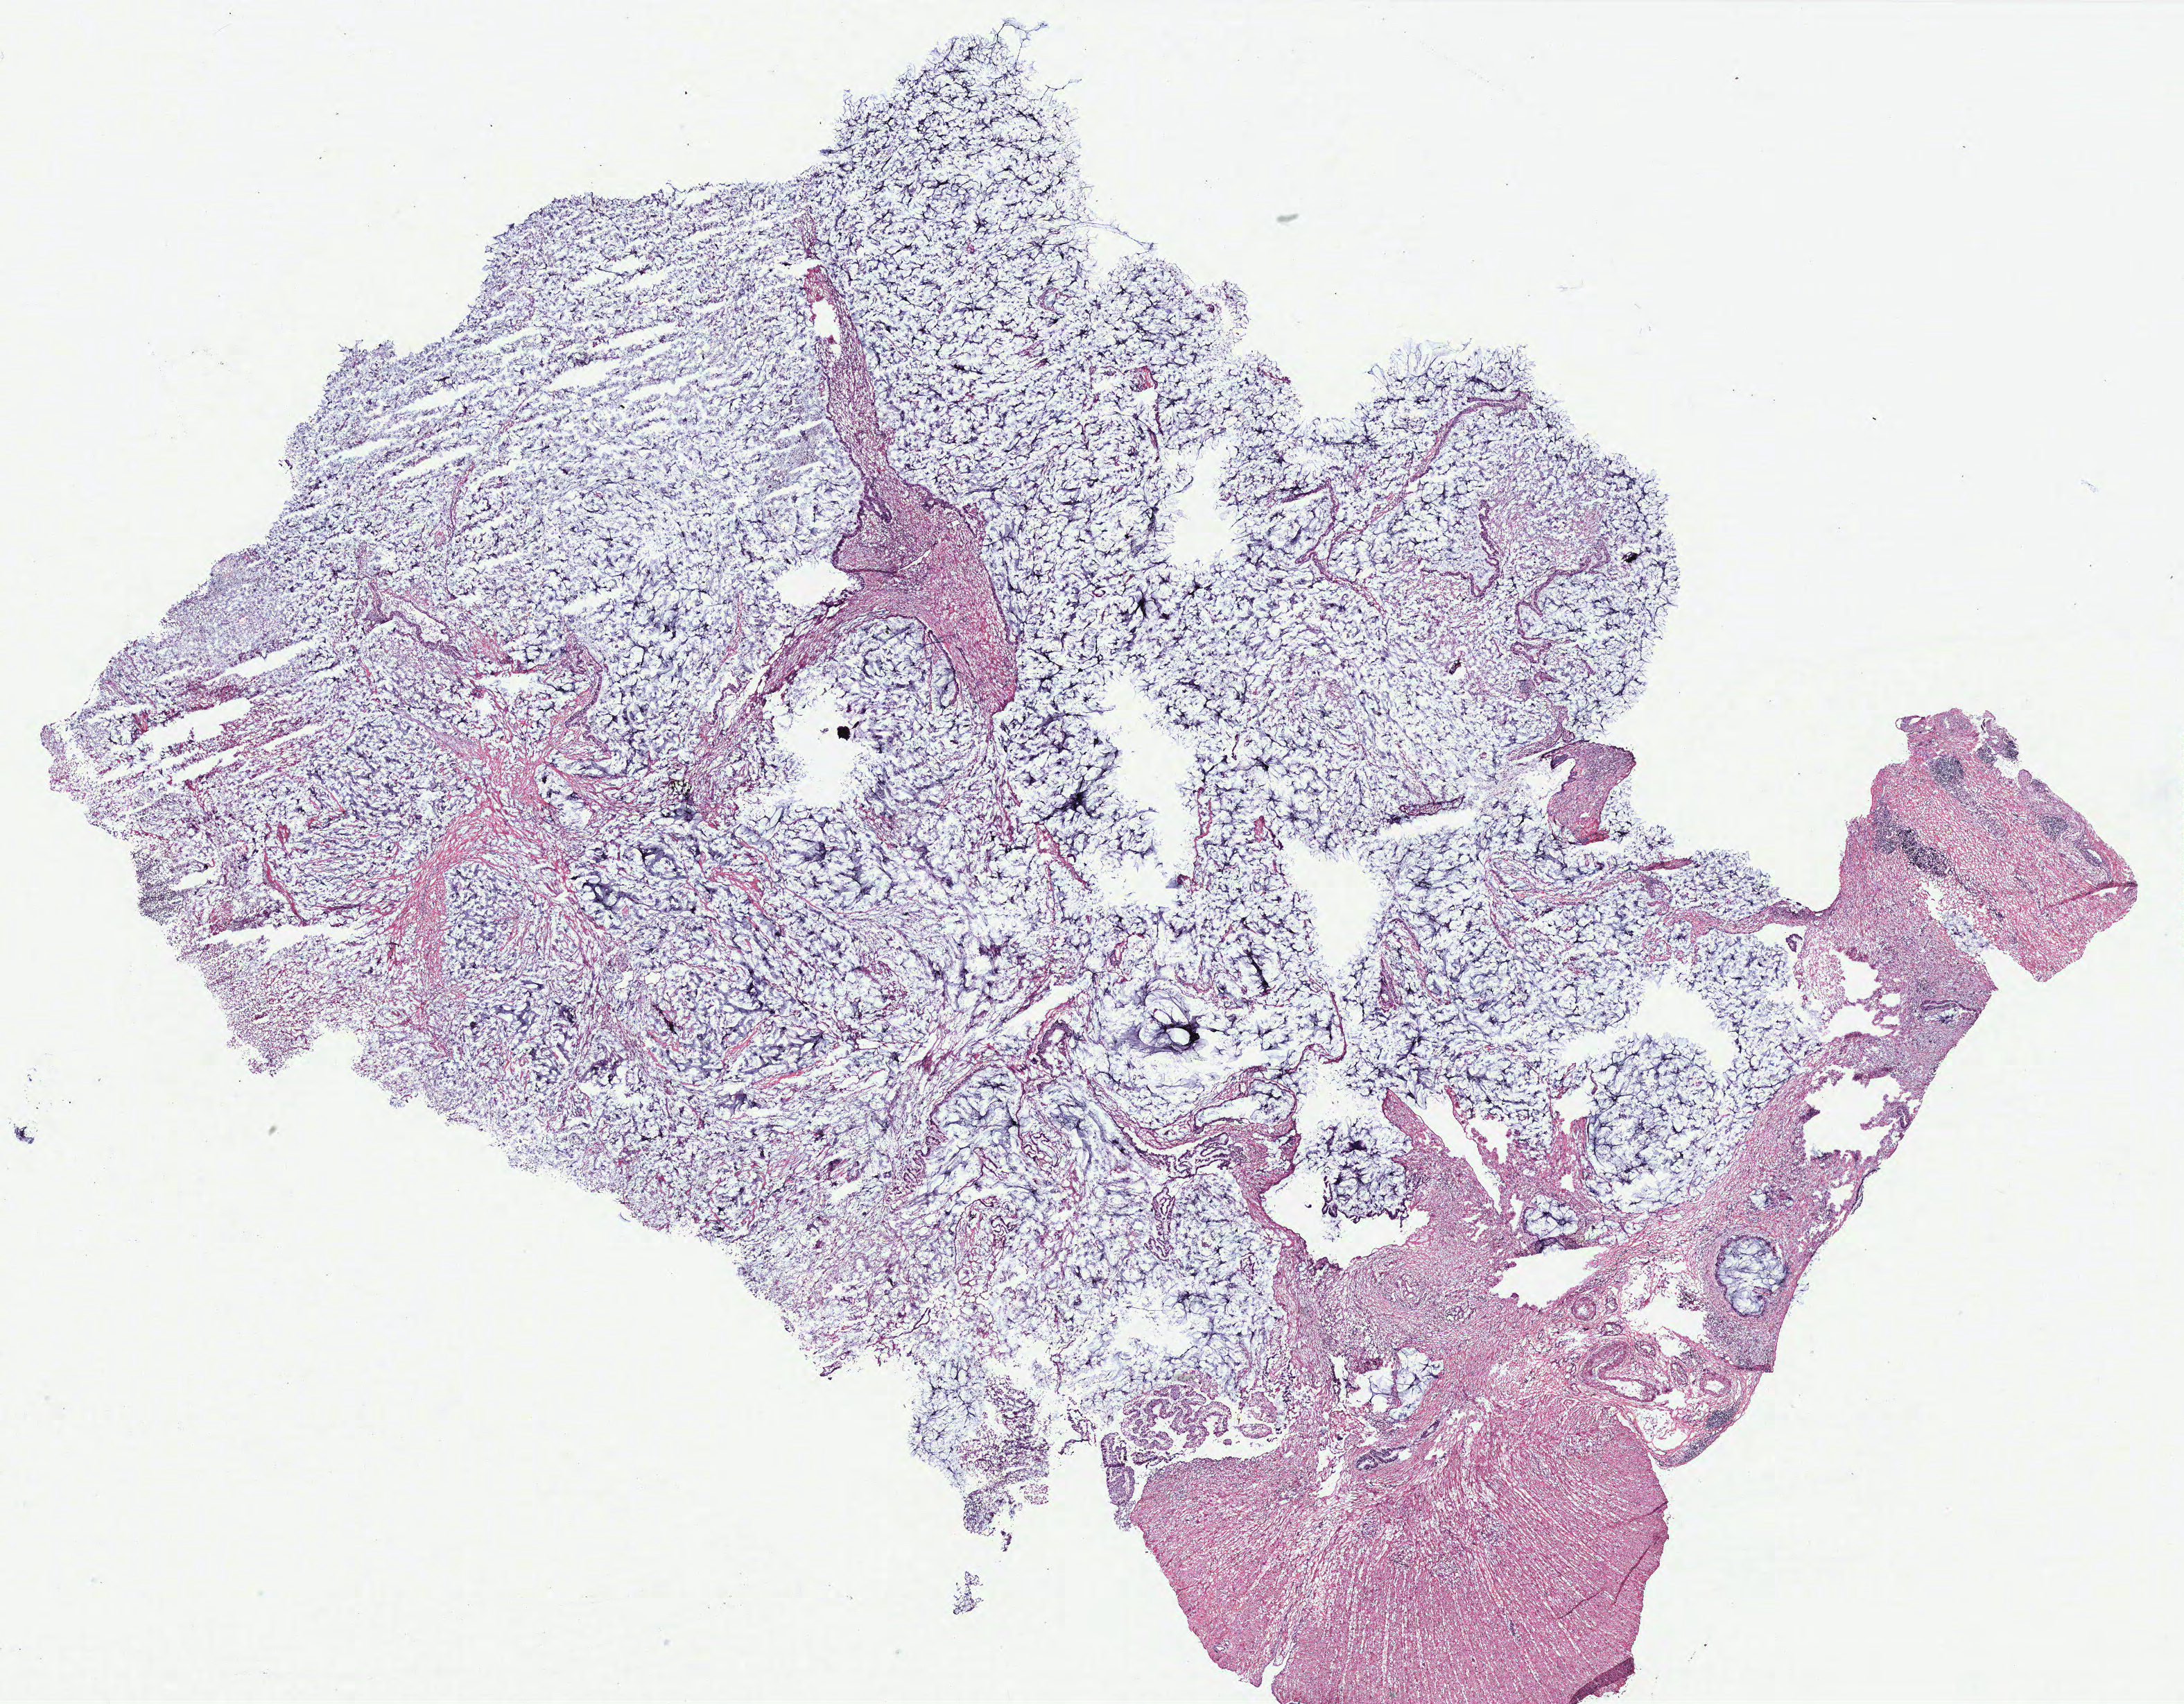
Whole-slide histology image, H&E, a low-resolution overview of the entire scanned area, about 25.2 x 19.7 mm, colon, tissue type not recorded.
Patient diagnosis (cohort enrolment): colon cancer (colon).